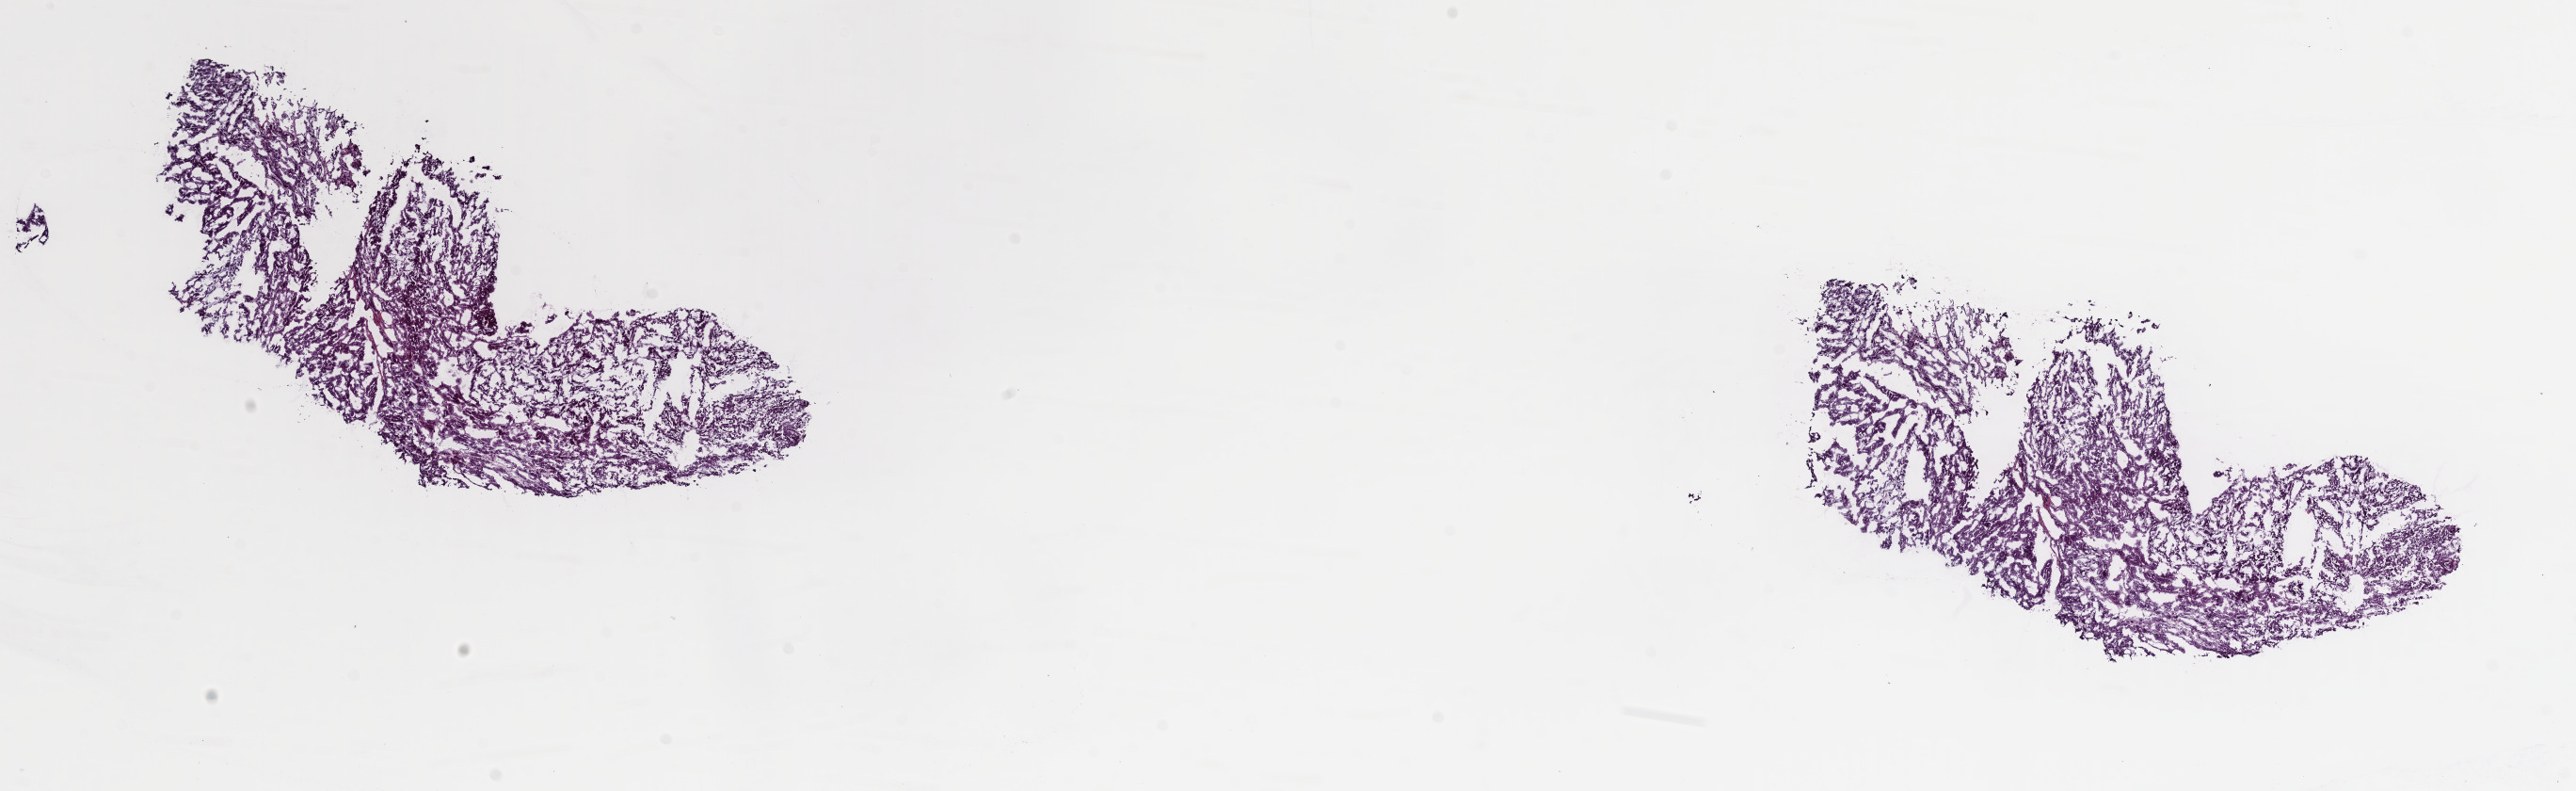
Digitized Hematoxylin and eosin (H&E) stained tissue section (whole slide), a low-resolution overview of the entire scanned area, about 21.6 x 6.6 mm. Frozen section. Adrenal cortex, primary tumour sample. Patient: female, age at initial diagnosis 56 years. Pathologist review of this section (percent, as recorded): tumour cells 100%, tumour nuclei 95%, normal cells 0%, stromal cells 0%, necrosis 0%. Infiltration values recorded for this section: lymphocyte infiltration 0%, monocyte infiltration 0%, neutrophil infiltration 0%.
• laterality: left
• histologic diagnosis: Adrenal cortical carcinoma (cortex of adrenal gland)